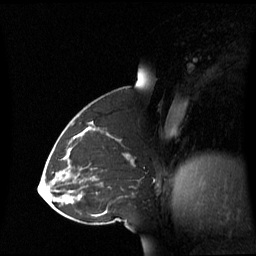
Breast MRI (dynamic contrast-enhanced), one sagittal slice; position 32 of 60 along the scan axis; dynamic contrast-enhanced series, image 2 of 3 at this slice position (ordered by acquisition); 1.5 T; TE 4.2 ms, TR 8.4 ms; 2.8 mm slice thickness; 256 × 256 image matrix, field of view 270 × 270 mm. Female patient, age 43 years. Case-level facts recorded for this patient, not image findings: setting: breast cancer imaged before/during neoadjuvant chemotherapy; receptor status: triple-negative.
Outlined on this slice (semi-automatically segmented with operator editing):
- analysis volume of interest (the breast-tissue region the enhancement analysis was run in; not a lesion): bounding box <69,137,135,198> (left, top, right, bottom; pixels)
- tumour enhancement mask (voxels above the 70 % enhancement threshold inside the analysis volume of interest): <73,137,128,156>